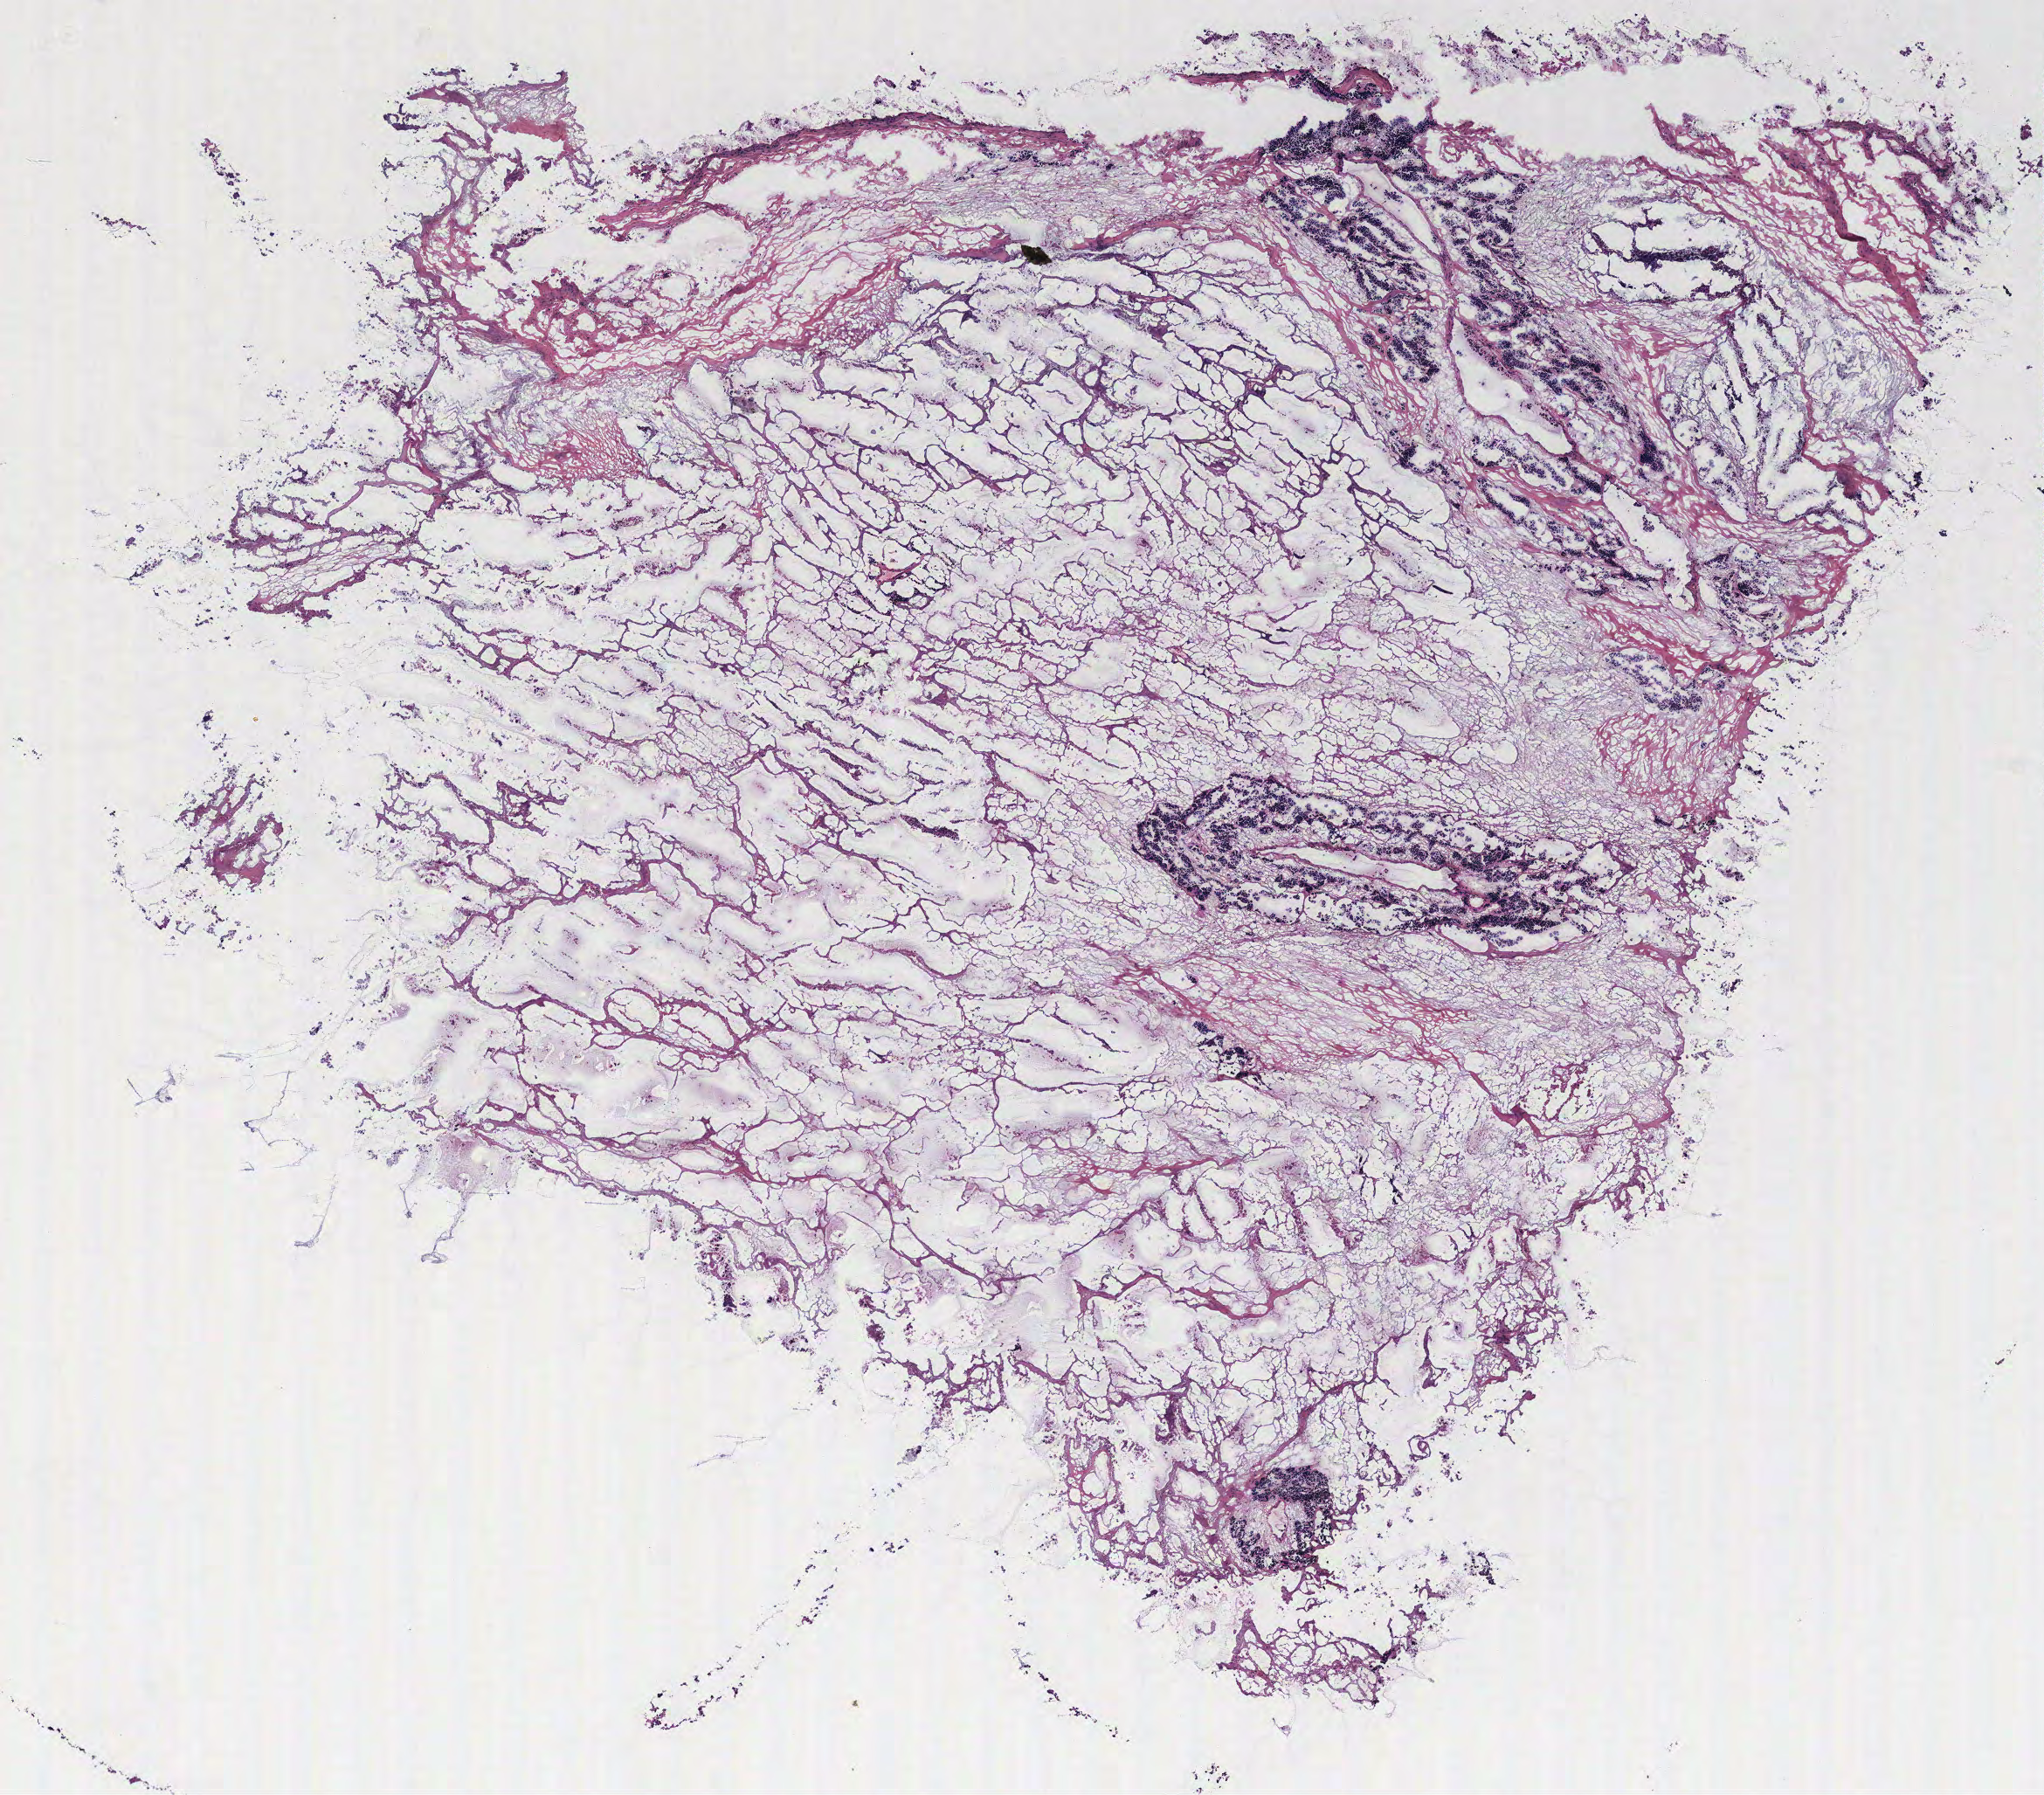
H&E-stained whole-slide image, shown as a low-resolution overview of the whole scanned area (about 9.4 x 8.2 mm); tumour tissue sample, ovary. Patient: female, age 57 years.
Diagnosis: Serous adenocarcinoma, NOS.